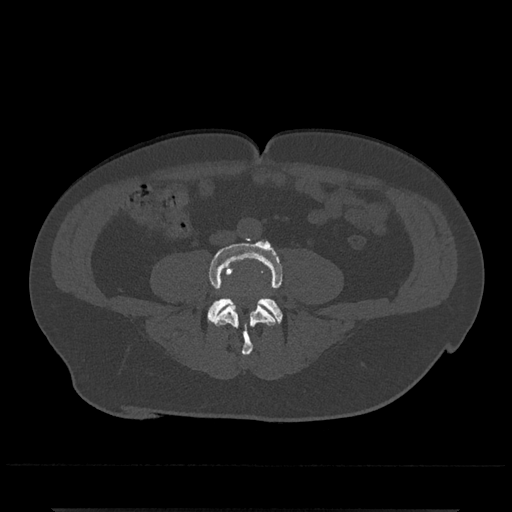
CT including the spine, one axial slice; position 128 of 797 along the scan axis; reconstruction kernel Br40s/3; 120 kVp; bone window (W 1800 / L 400 HU); 0.5 mm slice thickness; 512 × 512 image matrix, field of view 393 × 393 mm. Patient: male, 67 years. From the clinical record (not read from this slice): primary cancer: prostate.
Structures marked on this image (semi-automatic segmentation, software-assisted and operator-edited):
- L4 vertebra: bounding box <209,239,283,356> (left, top, right, bottom; pixels)
- L5 vertebra: <208,297,282,322>